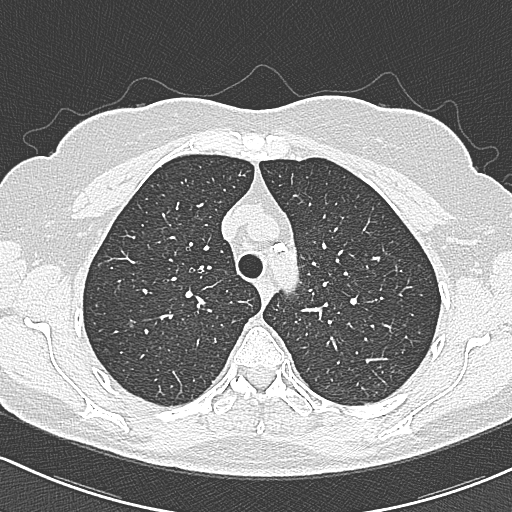
Chest CT (low-dose screening protocol), one axial image. Baseline screening round. Lung window (W 1500 / L -600 HU). 1 mm slice thickness. Lung (sharp) reconstruction kernel (B80f). 120 kVp. Slice 73 of 312 in the series. 512 × 512 image matrix, field of view 318 × 318 mm. Female, age 65 years at enrolment.
Expert-annotated lung lesion, box from (x=372, y=234) to (x=414, y=285) px. The screening reader recorded 3 non-calcified nodules or masses ≥4 mm on this exam (left upper lobe, left upper lobe, right upper lobe); which of them this box marks is not recorded. Later outcome: lung cancer diagnosed 390 days after this screen (after the second annual screen) — bronchiolo-alveolar carcinoma, non-mucinous, left upper lobe, stage IA (AJCC 6th edition), 10 mm at pathology.